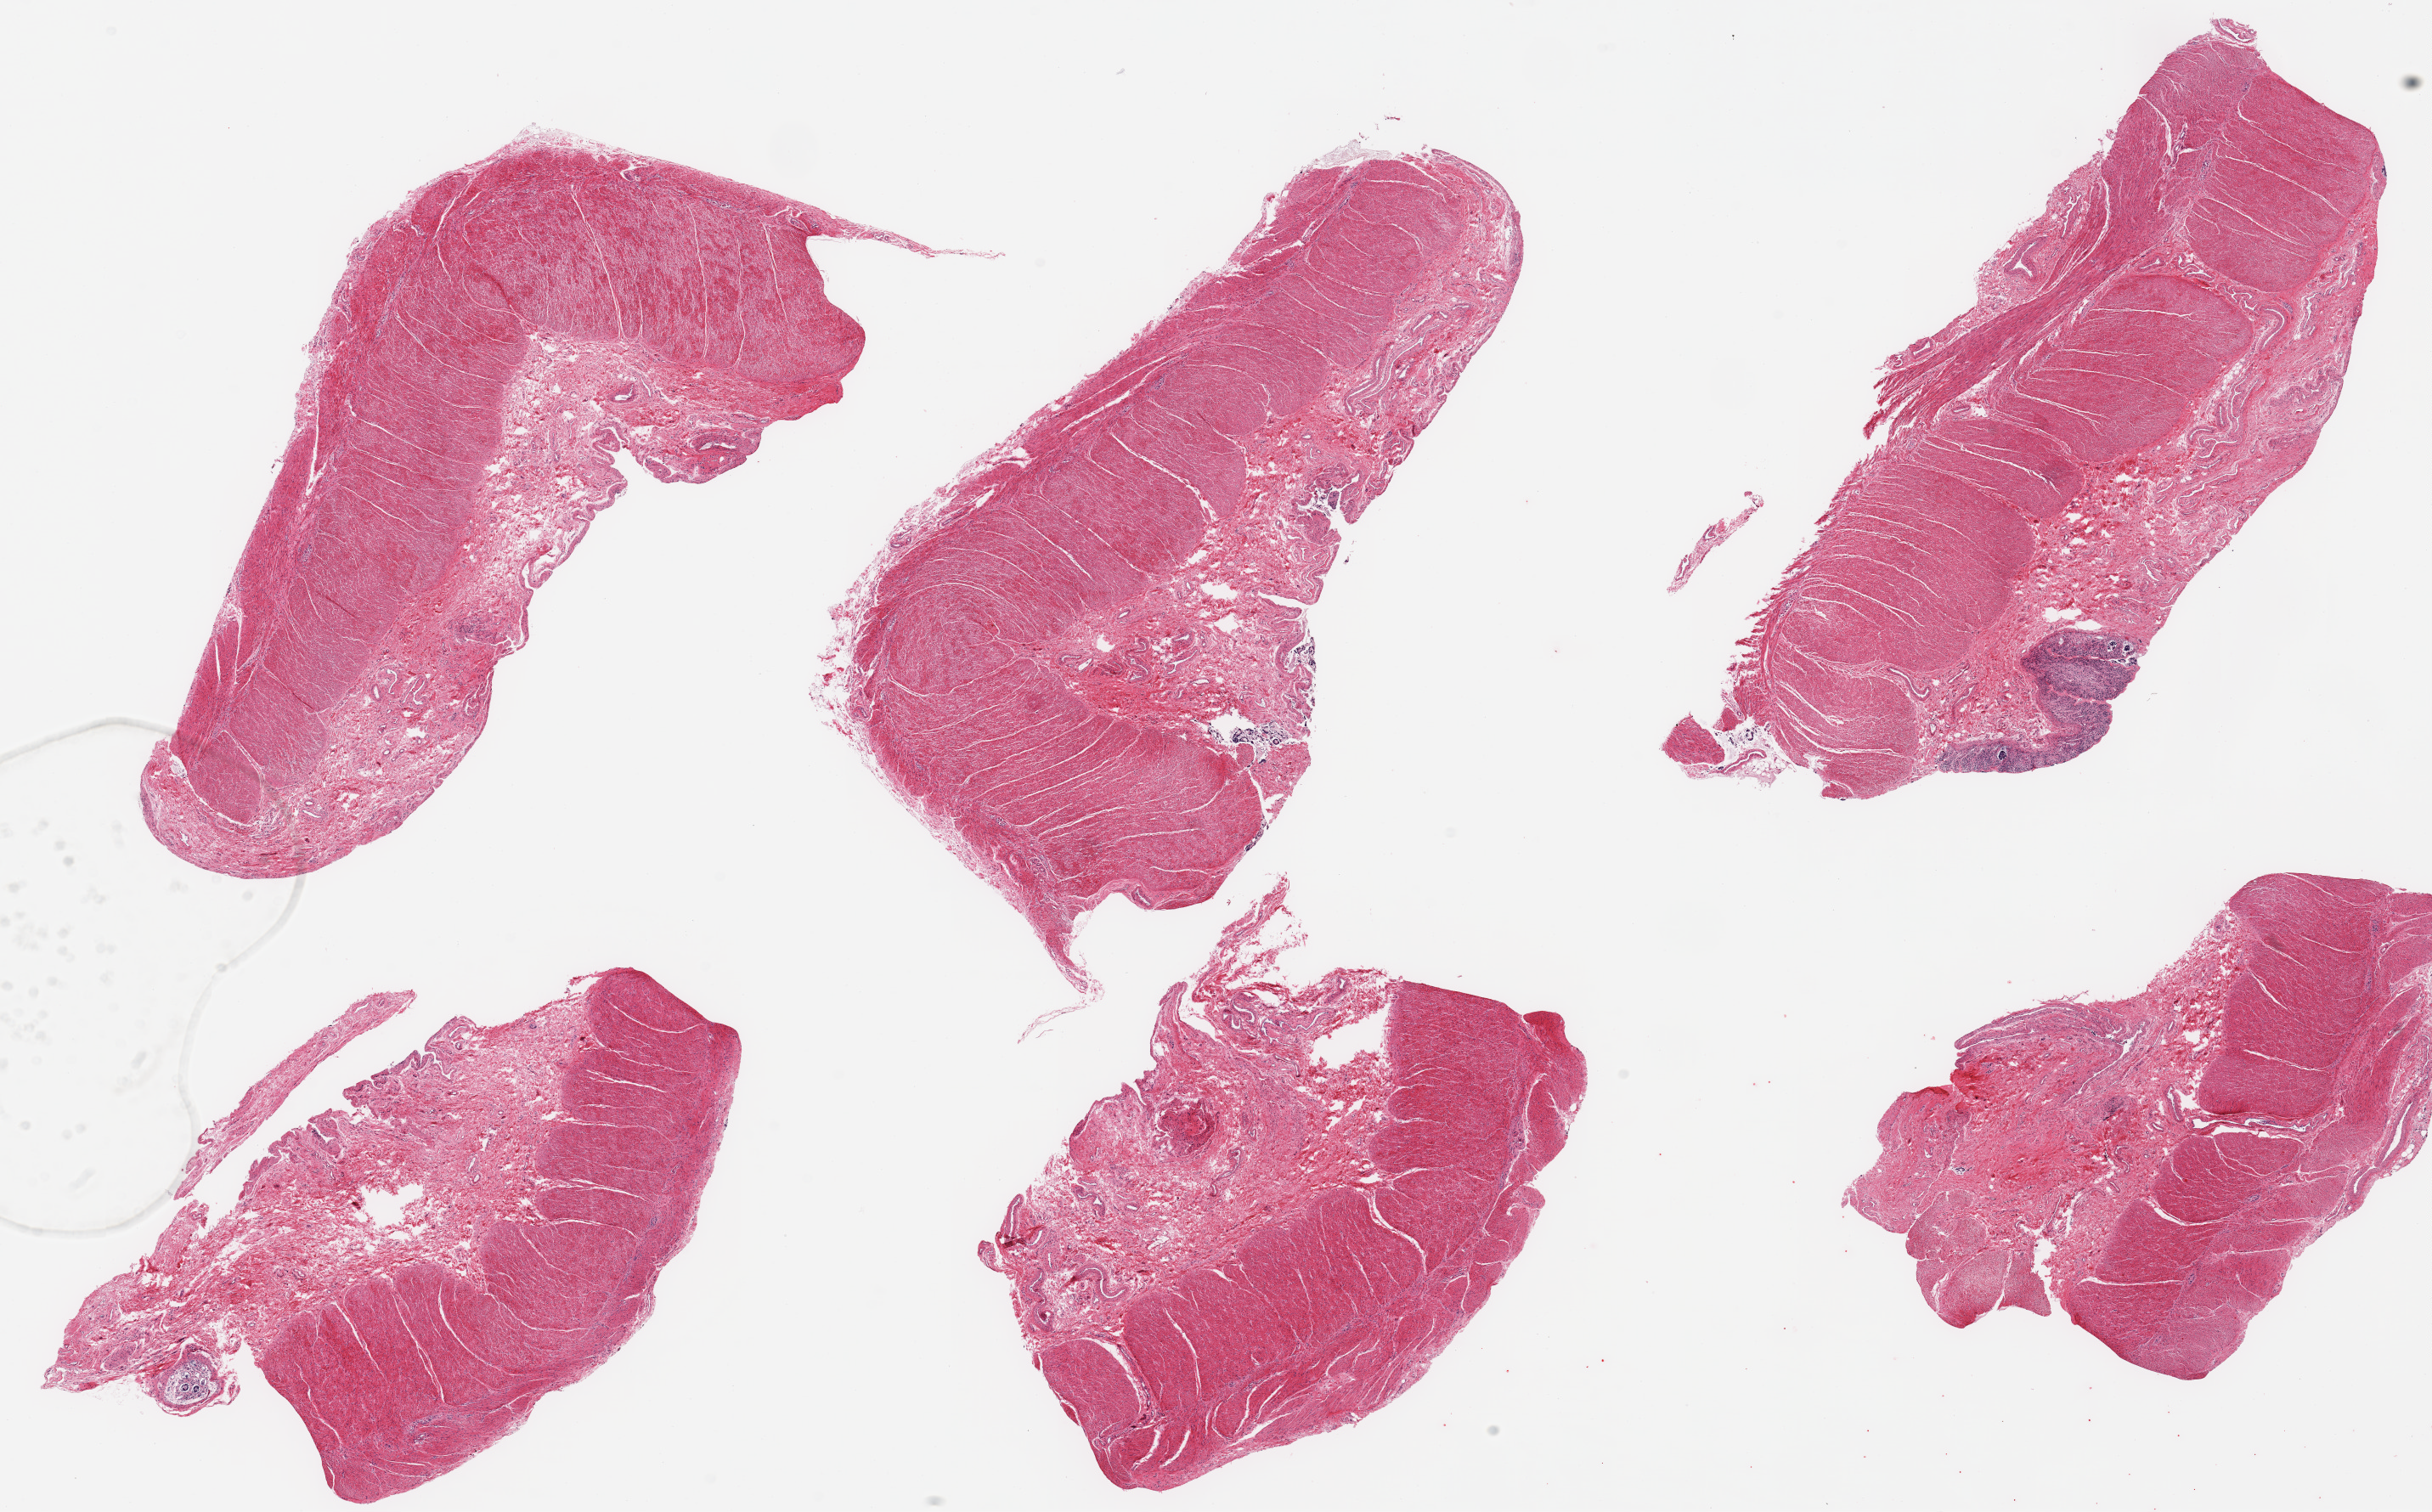
Digitized hematoxylin and eosin (H&E)-stained section — whole scanned area (about 22.6 x 14.1 mm, from a 20x scan) shown as a low-resolution overview, PAXgene-fixed, paraffin-embedded tissue, sampled site (target tissue): sigmoid colon, donor tissue sample. Donor sex: male.
Pathologist's review note for this sample: 6 pieces; target muscularis with one focal small fragment of moderately autolyzed colonic mucosa.